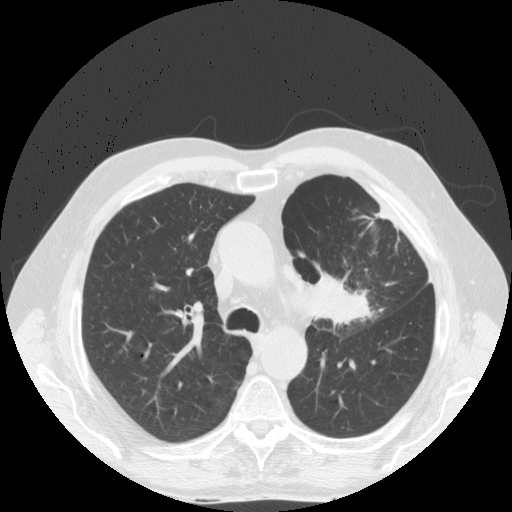
Low-dose screening chest CT, axial slice, baseline annual screen, lung window (W 1500 / L -600 HU), 2.5 mm slice thickness, standard (soft-tissue) reconstruction kernel (STANDARD), 140 kVp, 512 × 512 image matrix. Male, age 70 years at enrolment. Former smoker at enrolment.
Expert reader's lesion annotation, bounding box (x1, y1, x2, y2) in pixels: (293, 255, 388, 344). The exam's reader record, not a measurement of the box and not confirmed to be the same lesion: non-calcified nodule or mass ≥4 mm, left upper lobe, 46 × 31 mm, spiculated (stellate) margins, soft tissue attenuation. Official screen result: positive, change unspecified: nodule(s) >= 4 mm or enlarging nodule(s), mass(es), or other non-specific abnormalities suspicious for lung cancer.